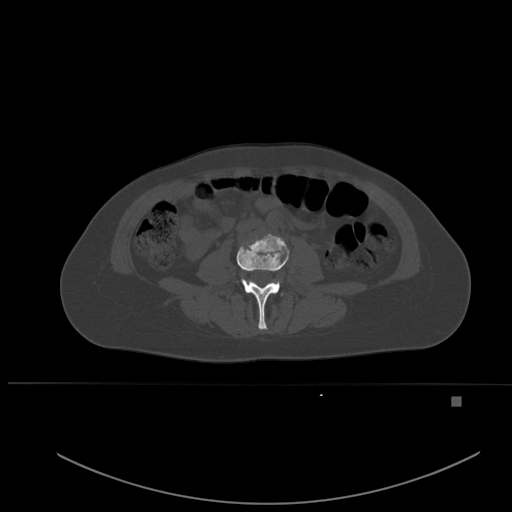
CT including the spine, one axial slice; position 189 of 651 along the scan axis; bone window (W 1800 / L 400 HU); 1.5 mm slice thickness; 512 × 512 image matrix. Patient: female, 49 years. From the clinical record (not read from this slice): primary cancer: breast.
Structures marked on this image (semi-automatic segmentation, software-assisted and operator-edited):
- L3 vertebra: bounding box [x1, y1, x2, y2] px = [236, 234, 289, 330]